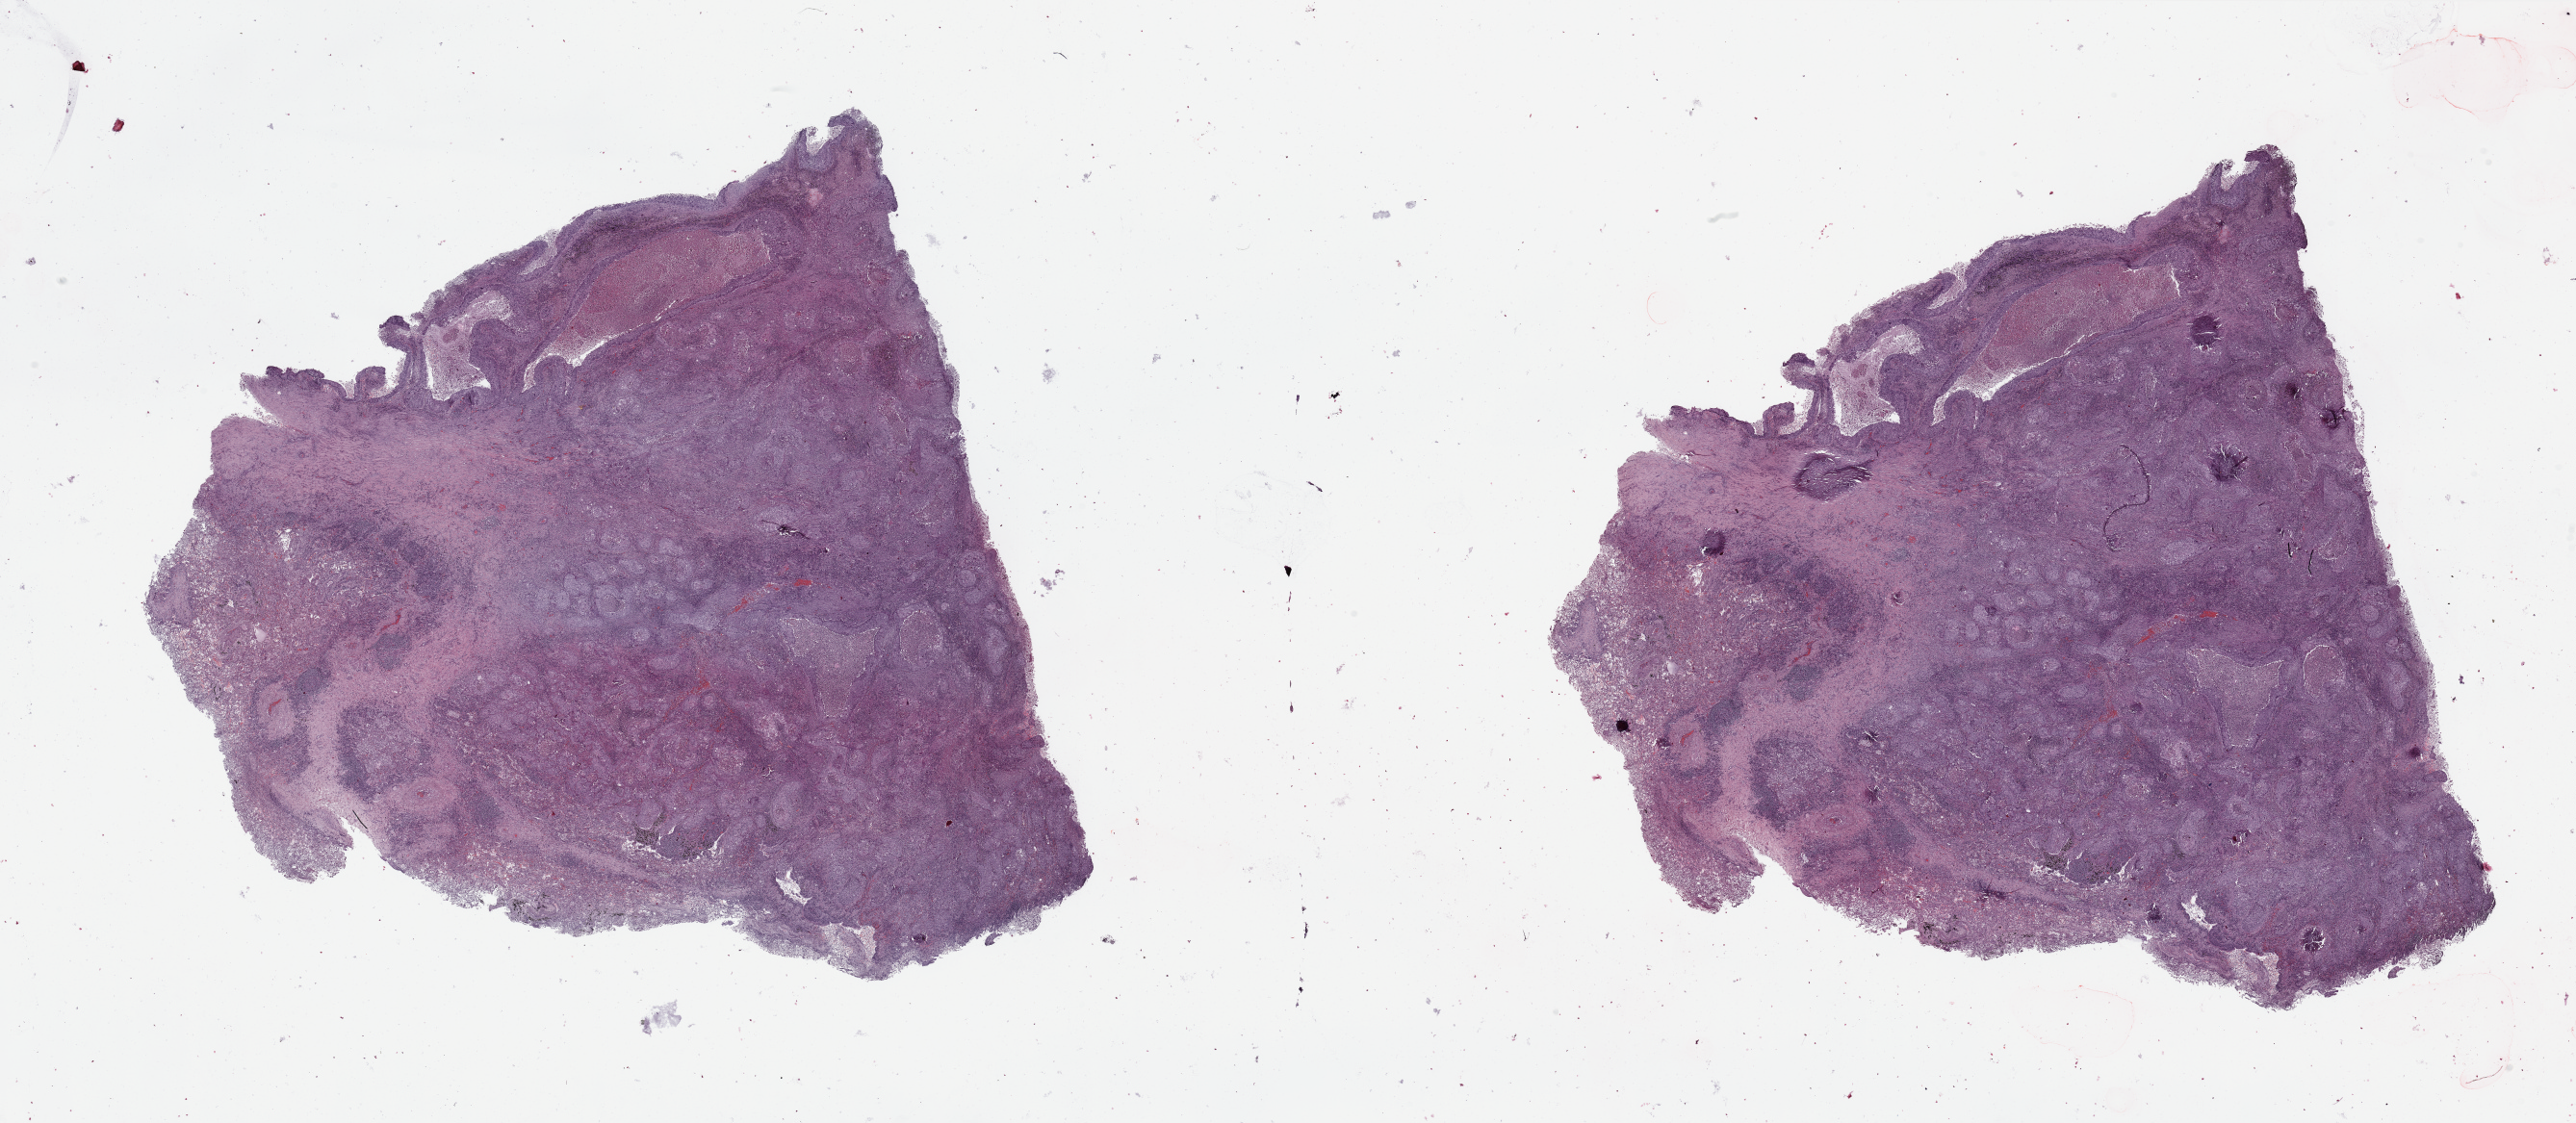
Hematoxylin and eosin (H&E) stained whole-slide image — whole scanned area (about 42.3 x 18.5 mm) shown as a low-resolution overview; lung, tumour tissue. 70-year-old male patient. Histologic grade: G2 (moderately differentiated).
- AJCC pathologic stage: IB
- primary tumour site (as recorded): left lower lobe
- diagnosis: Squamous cell carcinoma, NOS